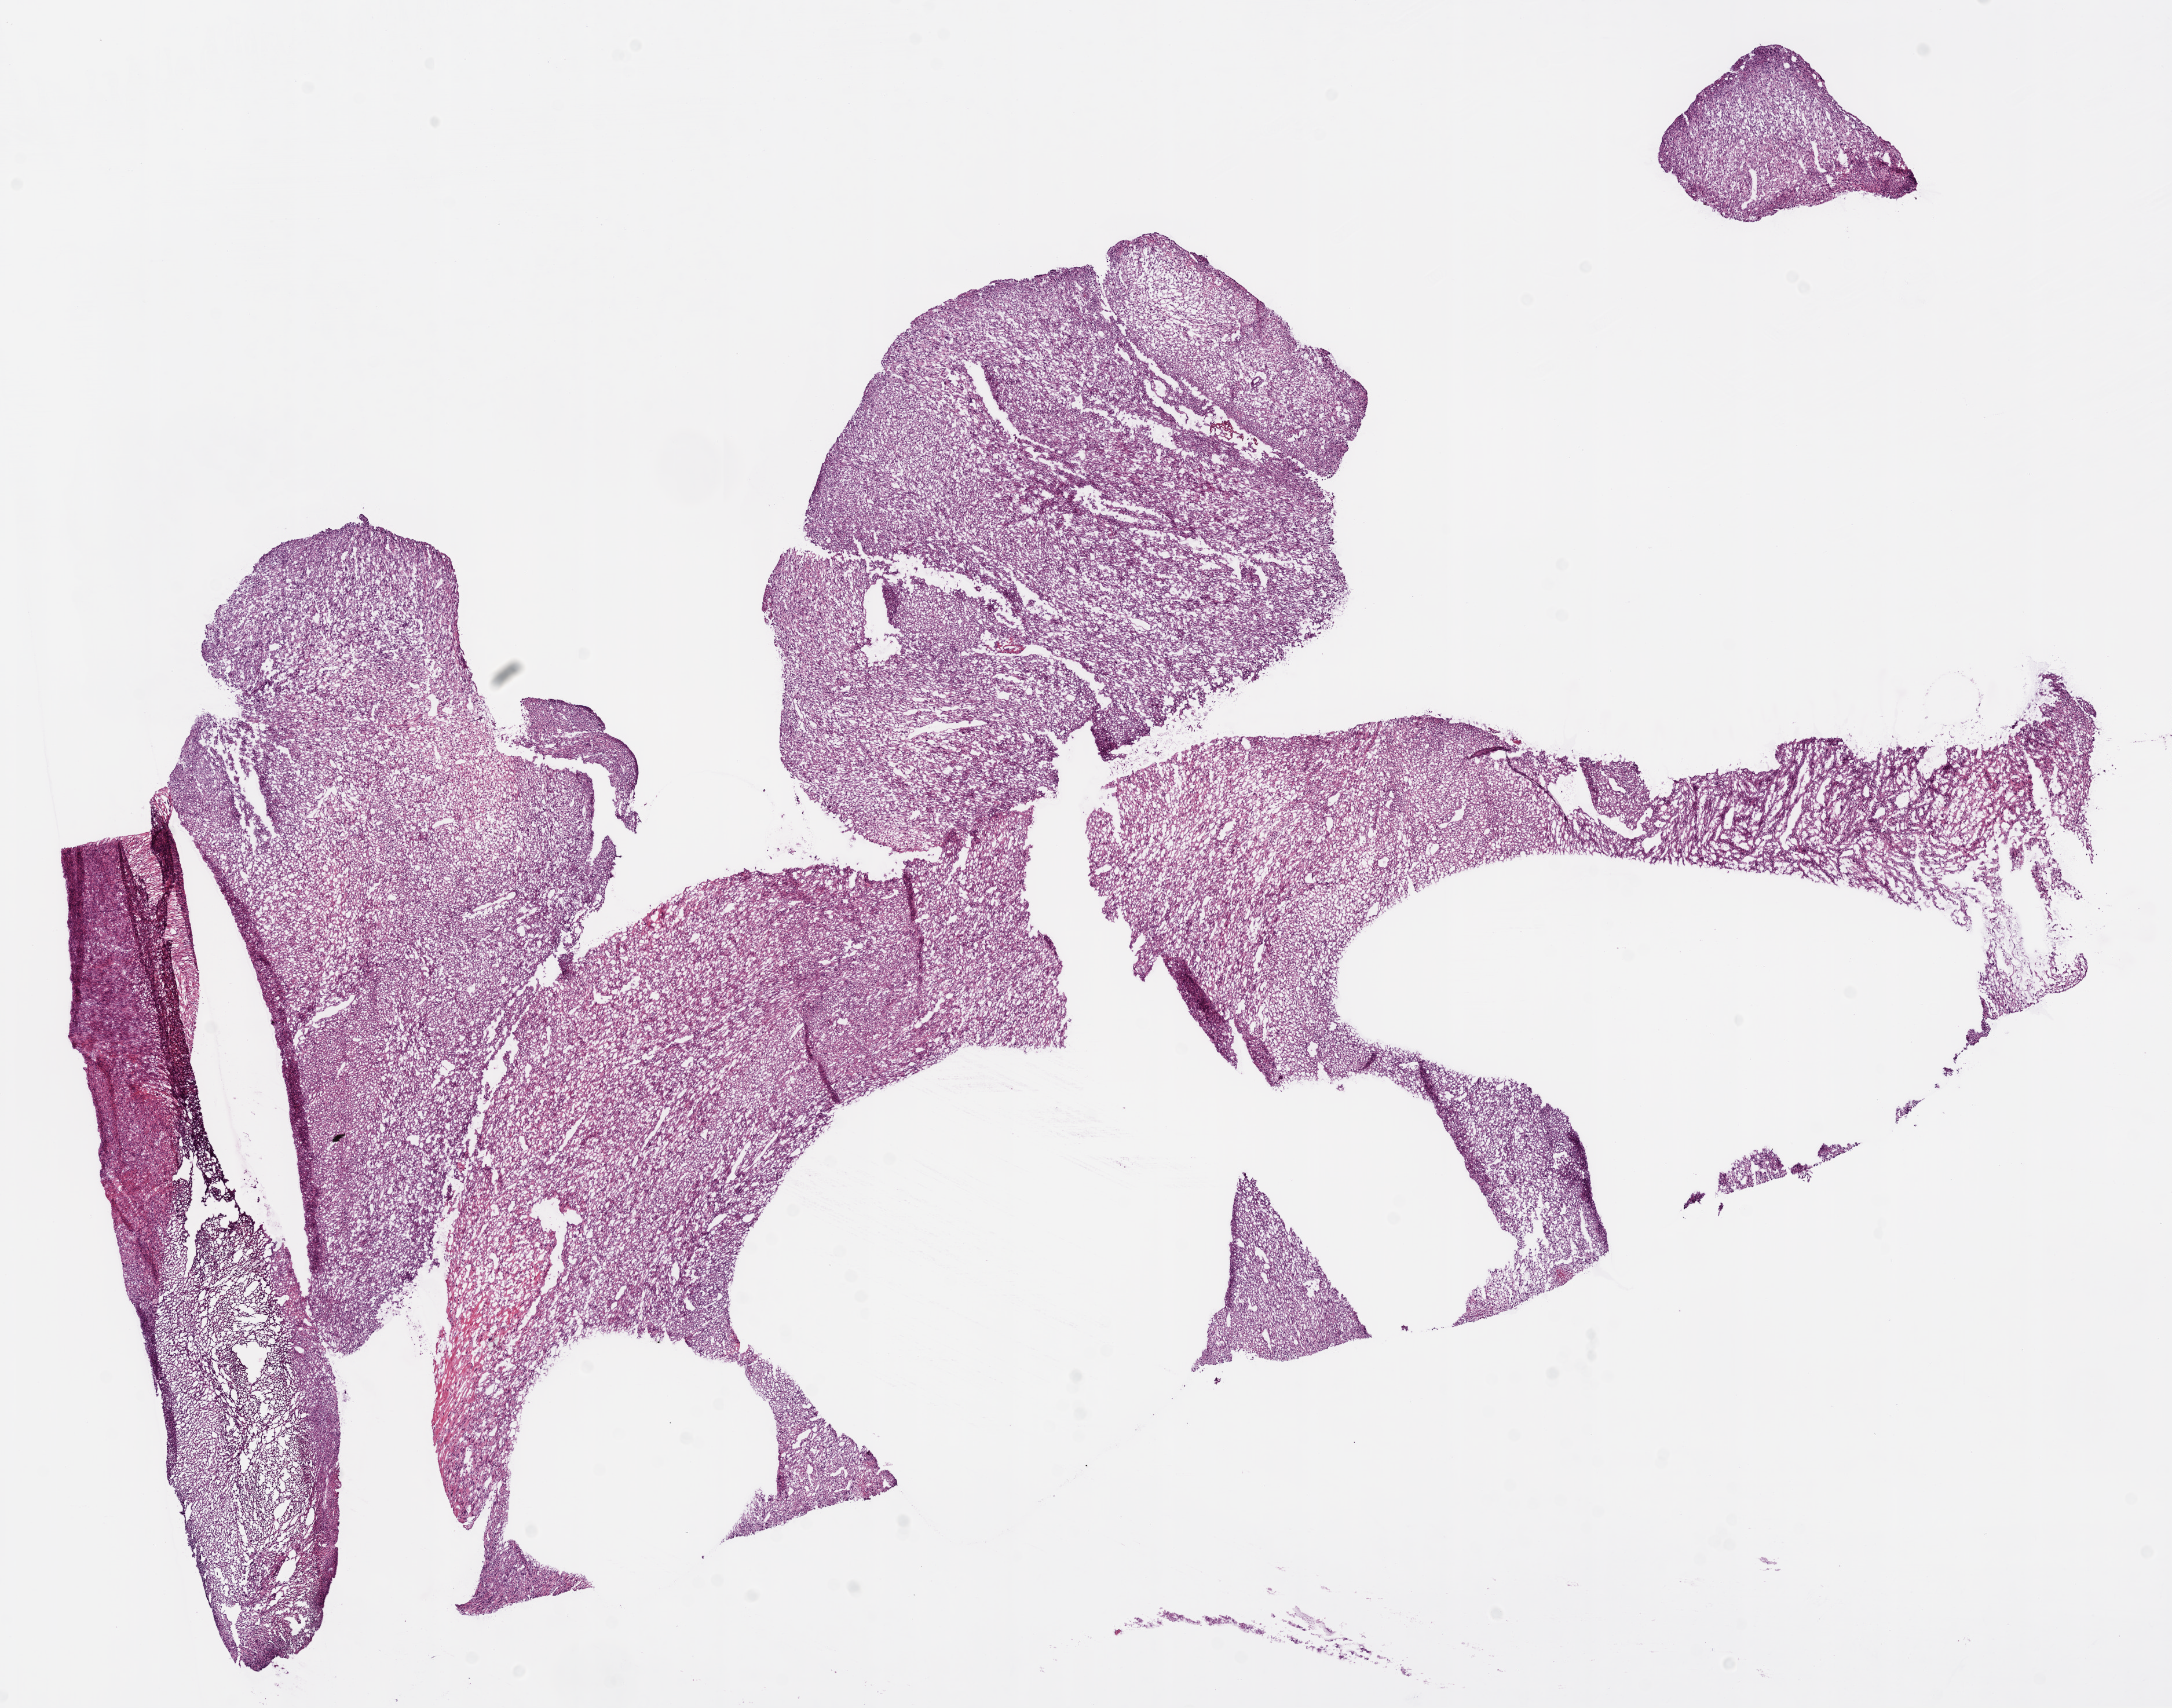
H&E-stained whole-slide image, shown as a low-resolution overview of the whole scanned area (about 15.0 x 11.8 mm, acquisition: 20x scan); frozen section from the bottom of the tissue portion; sample: primary tumour, kidney. Patient: female, age at initial diagnosis 73 years. Histologic grade: G4 (undifferentiated). Slide review estimates, as recorded: tumour cells 100%, tumour nuclei 95%, normal cells 0%, stromal cells 0%, necrosis 0%. Infiltration values recorded for this section: lymphocyte infiltration 1%, monocyte infiltration 0%, neutrophil infiltration 0%.
Histologic diagnosis: Clear cell adenocarcinoma, NOS. AJCC pathologic stage: IV. Laterality: left.